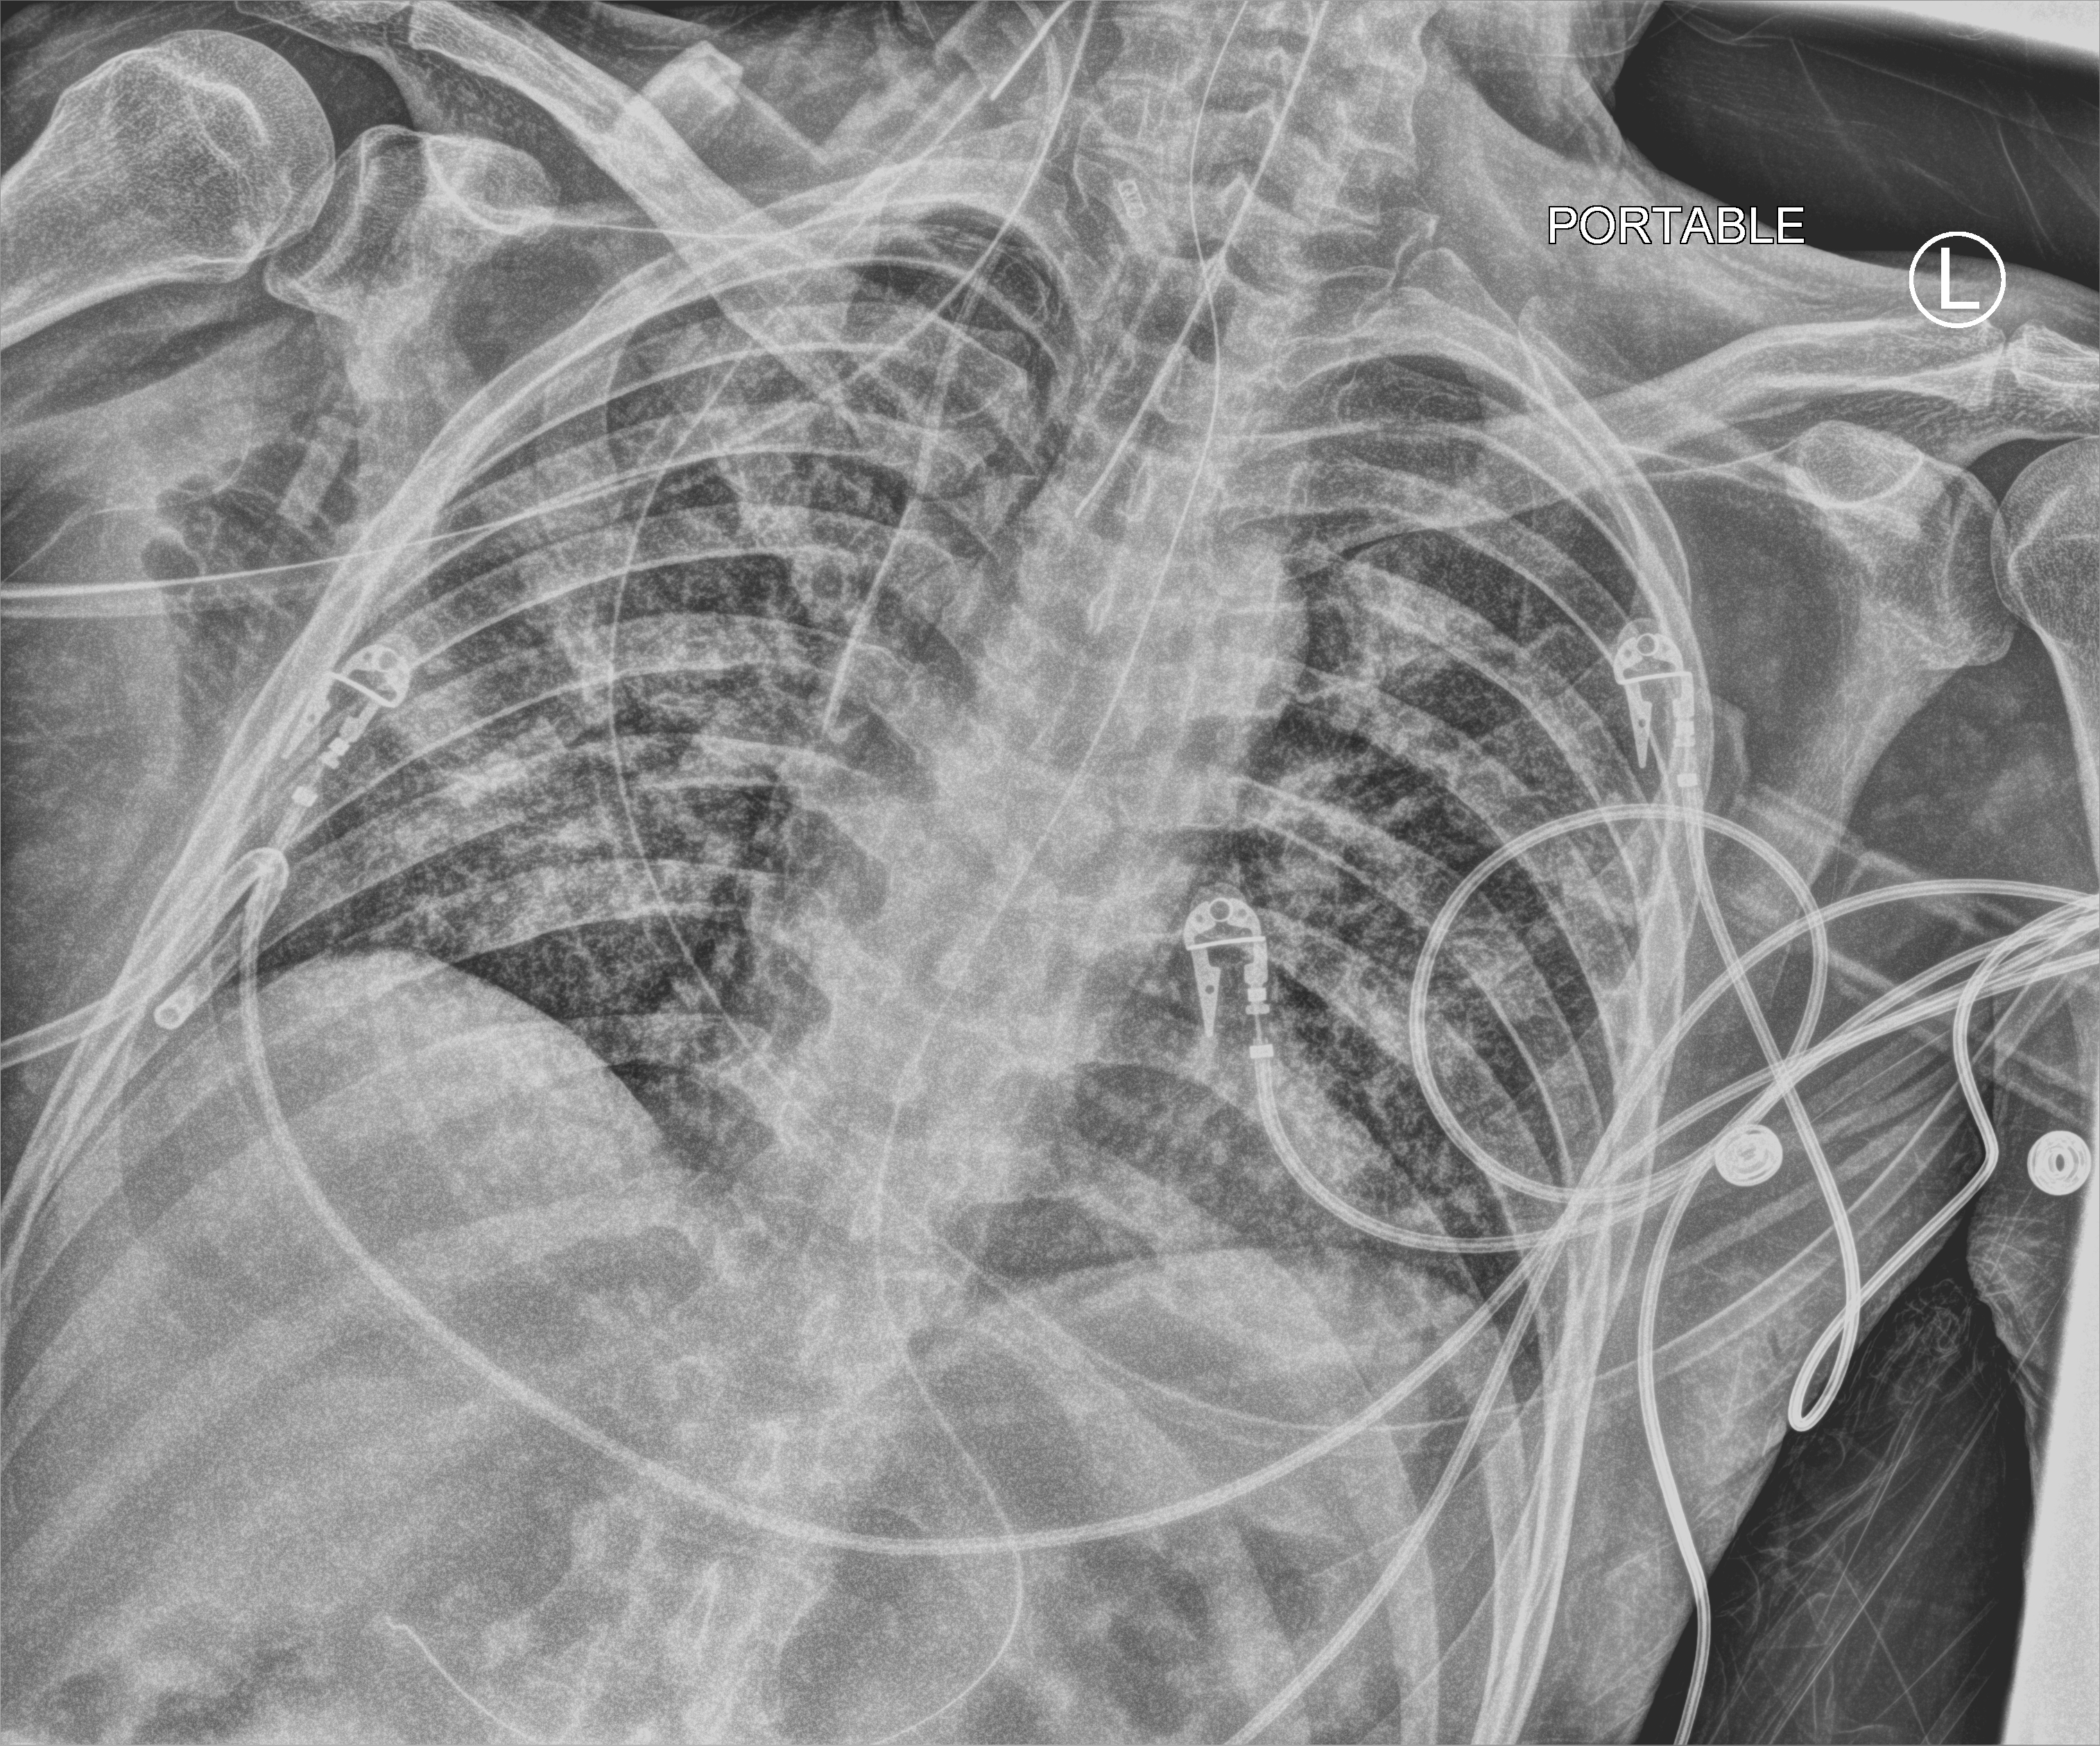
Portable chest radiograph. Male patient hospitalised with COVID-19, age 18–59 years.
From the hospital-stay record, not from the radiograph (when in the stay this image was taken is not recorded):
- diabetes (admission record): no